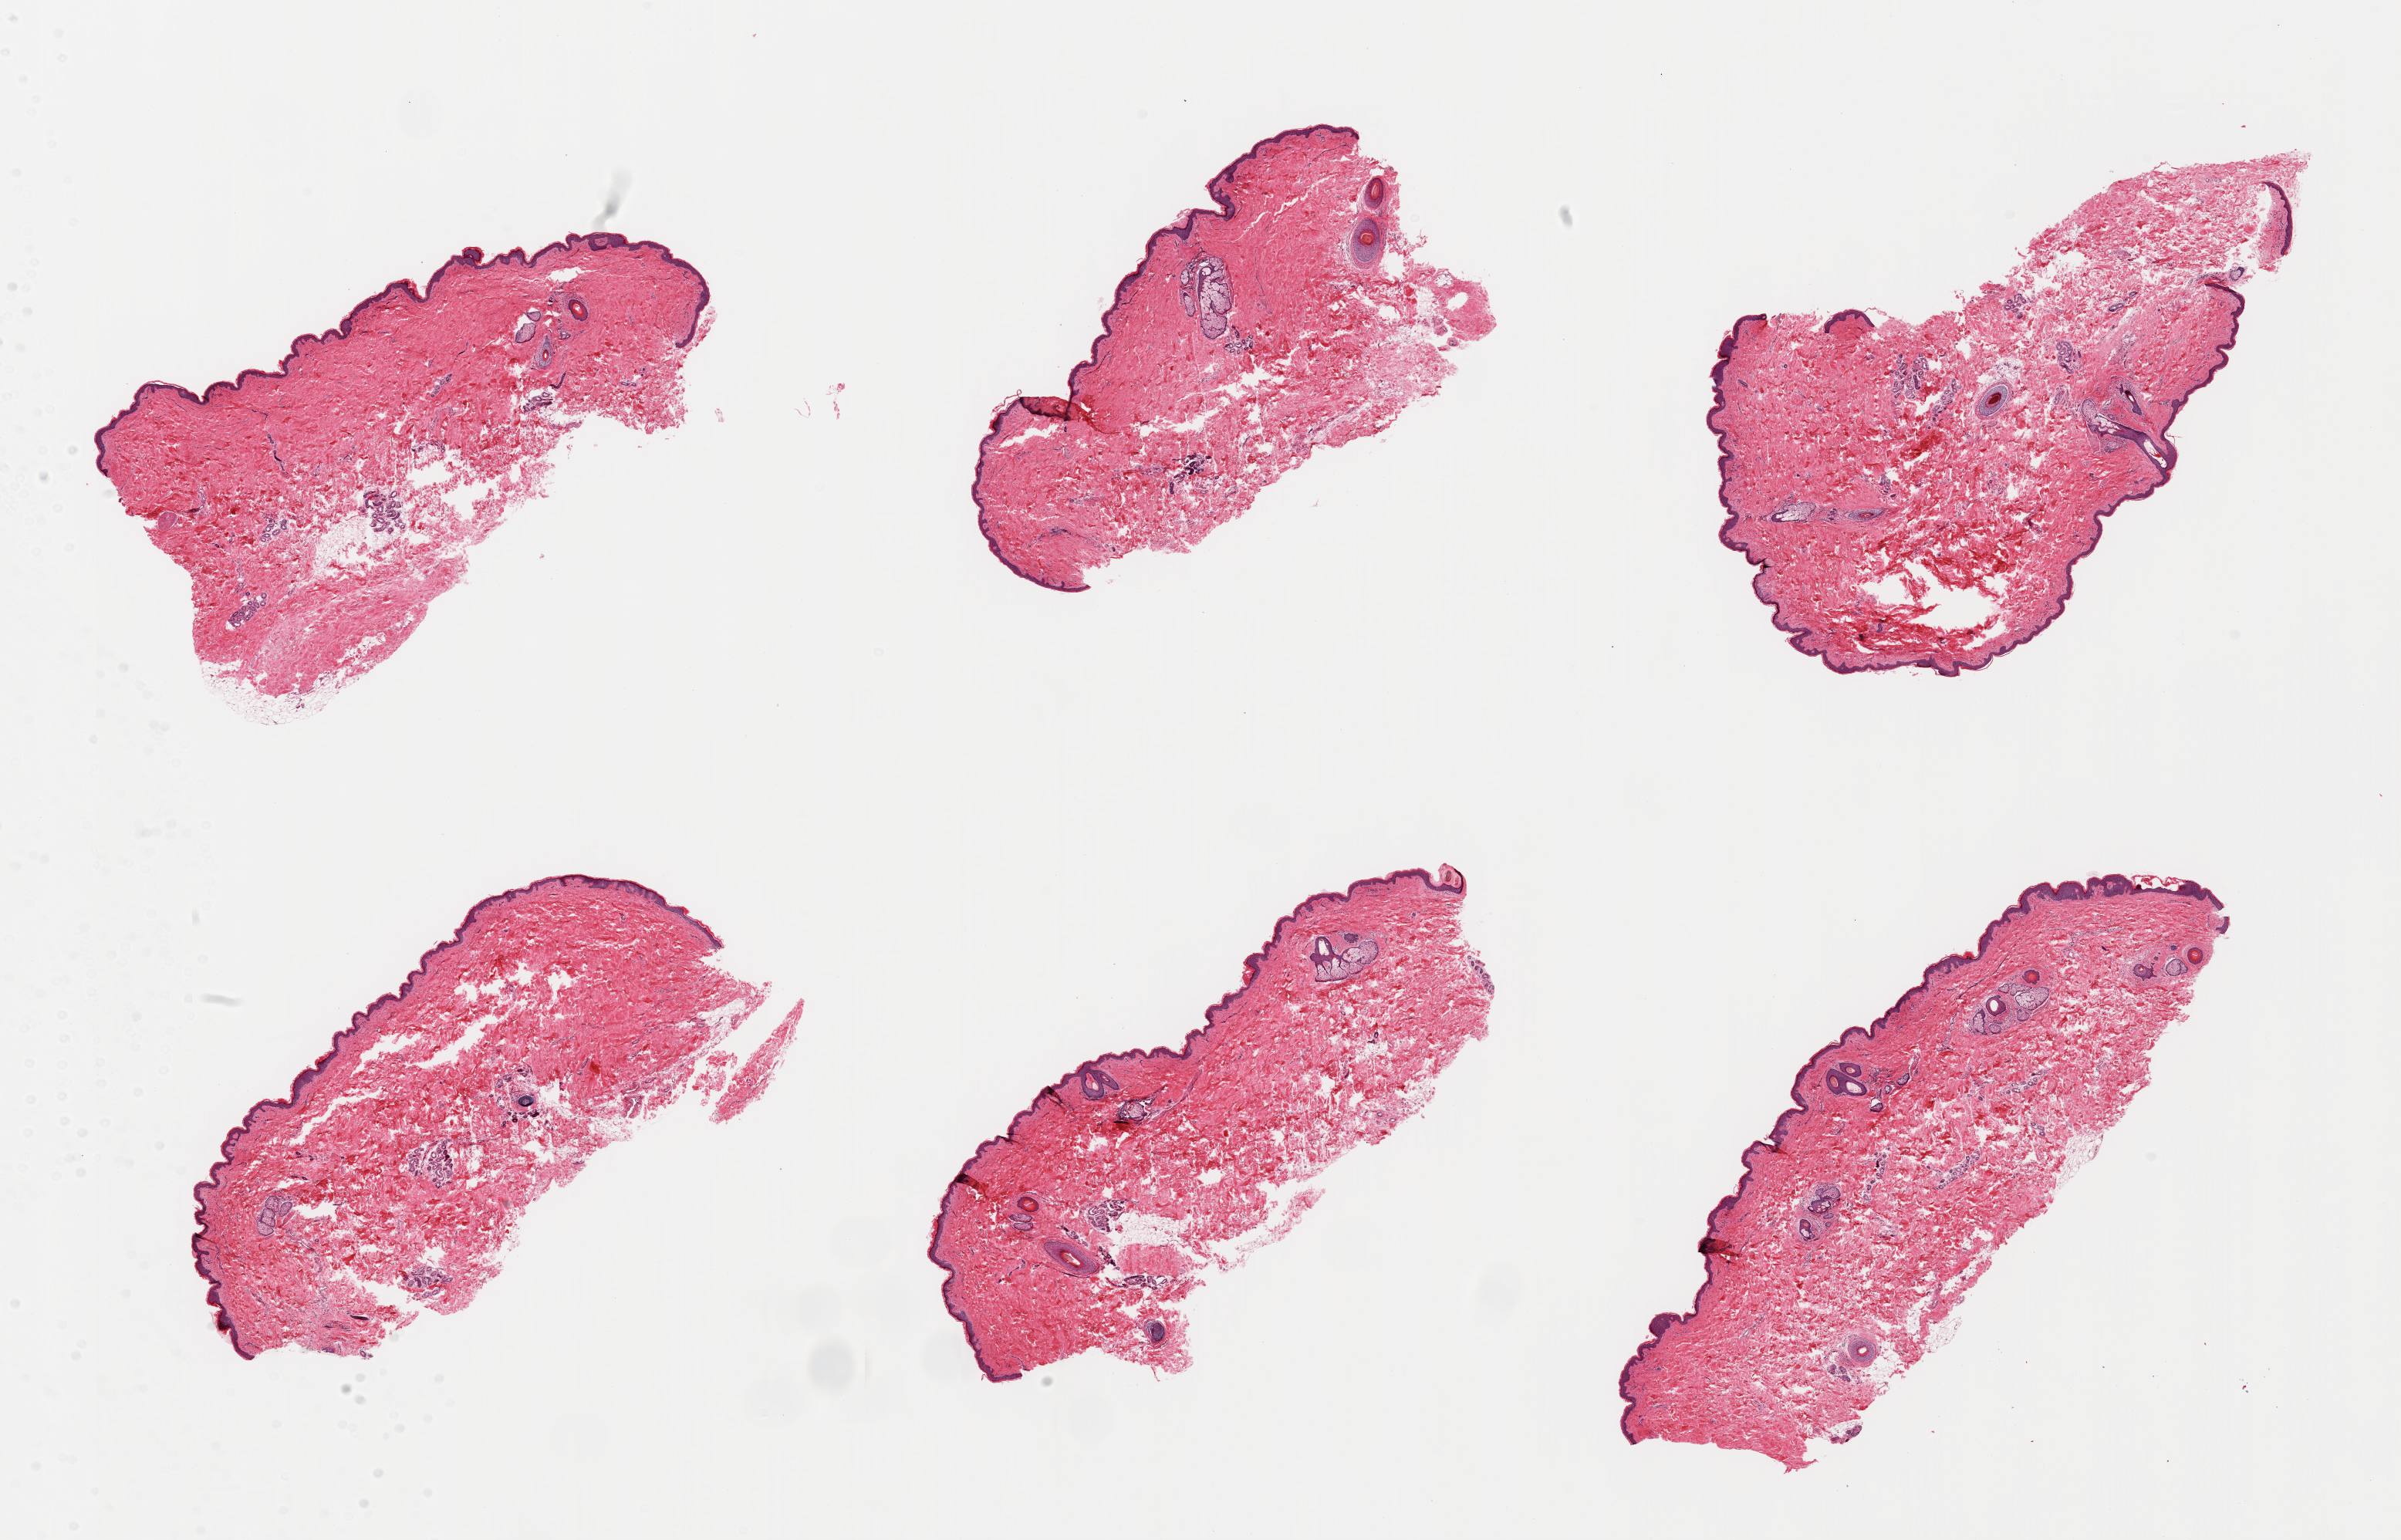
Digitized hematoxylin and eosin (H&E)-stained section, brightfield, shown as a low-resolution overview of the whole scanned area (about 24.6 x 15.8 mm). PAXgene-fixed, paraffin-embedded tissue. Section of skin of suprapubic region (target tissue). Donor tissue sample. Donor: male.
Pathologist's review note for this sample: 6 pieces, squamous epithelium is ~50 microns; minimal adherent dermal fat.